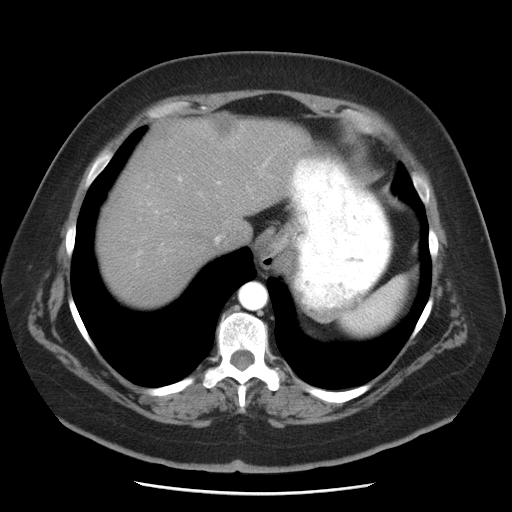
Contrast-enhanced abdominal CT, one axial slice. Slice 40 of 55 in the series (ordered by position). 120 kVp. Intravenous contrast given. Soft-tissue window (W 400 / L 40 HU). 5 mm slice thickness. 512 × 512 image matrix. Female patient, age 52 years. From the clinical record (not read from this slice): diagnosis: colorectal cancer liver metastases, imaged before liver resection; multiple liver metastases: yes.
Annotated regions visible in this slice (manually delineated by an expert):
- hepatic veins: bounding box (x1, y1, x2, y2) in pixels: (215, 236, 221, 242)
- liver: (95, 114, 312, 309)
- planned liver remnant (the part of the liver to remain after resection): (95, 167, 204, 309)
- portal vein (with intrahepatic branches): (149, 176, 221, 204)
- liver metastasis: (208, 113, 241, 141)